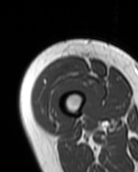
MRI of an extremity soft-tissue mass, one axial slice. Position 16 of 99 along the scan axis. MR volume resampled by the dataset authors to the PET/CT grid (not the native acquisition matrix). 3.27 mm slice thickness. 138 × 172 image matrix, field of view 135 × 168 mm. Female patient. Case-level facts recorded for this patient, not image findings: histological type: pleiomorphic undifferentiated sarcoma; grade: high; site of the primary tumour: right quadricep.
Annotated regions visible in this slice (expert contour drawn on MRI and transferred to this co-registered scan by the dataset authors):
- gross tumour volume including surrounding oedema: box from (x=32, y=57) to (x=88, y=119) px